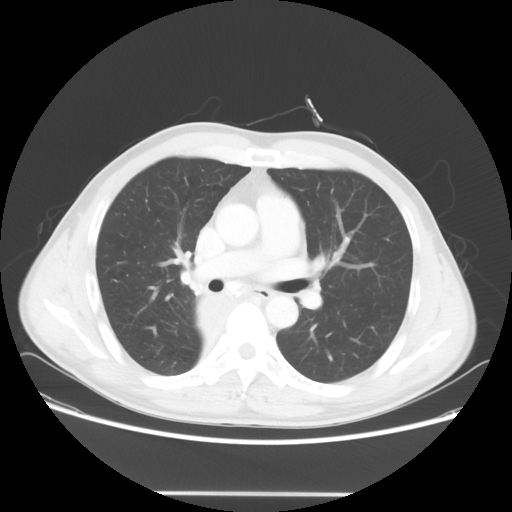
Chest CT, one axial slice. Position 36 of 62 along the scan axis. 120 kVp. Lung window (W 1500 / L -600 HU). 512 × 512 image matrix, field of view 393 × 393 mm. Patient: male, 47 years. From the clinical record (not read from this slice): clinical TNM (as recorded): T2 N0 M0; histopathological grade: G2.
Annotated regions visible in this slice (bounding box drawn by a radiologist):
- lung tumour (recorded histology: squamous cell carcinoma): bounding box <172,282,241,342> (left, top, right, bottom; pixels)